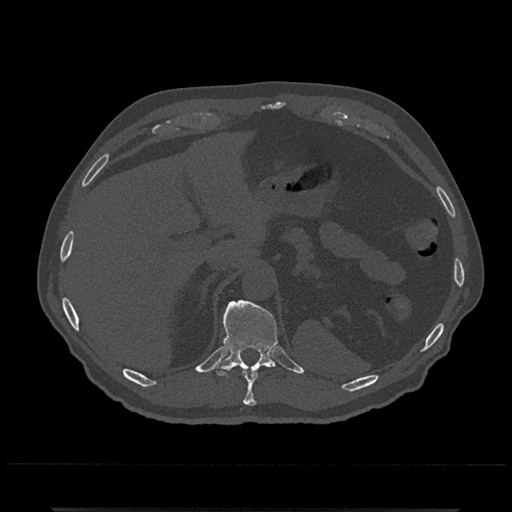
CT including the spine, one axial slice. Slice 510 of 797 in the series (ordered by position). Reconstruction kernel Br40s/3. Bone window (W 1800 / L 400 HU). 512 × 512 image matrix, field of view 393 × 393 mm. Patient: male, 67 years. From the clinical record (not read from this slice): primary cancer: prostate.
Structures marked on this image (semi-automatic segmentation, software-assisted and operator-edited):
- T10 vertebra: bounding box (x1, y1, x2, y2) in pixels: (243, 371, 258, 406)
- T11 vertebra: (214, 300, 278, 377)